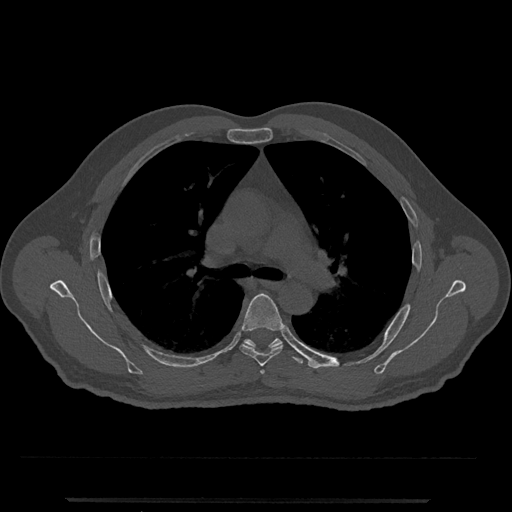
CT including the spine, one axial slice. Position 777 of 797 along the scan axis. Reconstruction kernel Br40s/3. 120 kVp. Bone window (W 1800 / L 400 HU). 0.5 mm slice thickness. 512 × 512 image matrix, field of view 419 × 419 mm. Patient: male, 63 years. From the clinical record (not read from this slice): primary cancer: prostate.
Structures marked on this image (semi-automatically segmented with operator editing):
- T5 vertebra: bounding box (x1, y1, x2, y2) in pixels: (239, 293, 283, 366)
- T6 vertebra: (244, 338, 304, 365)